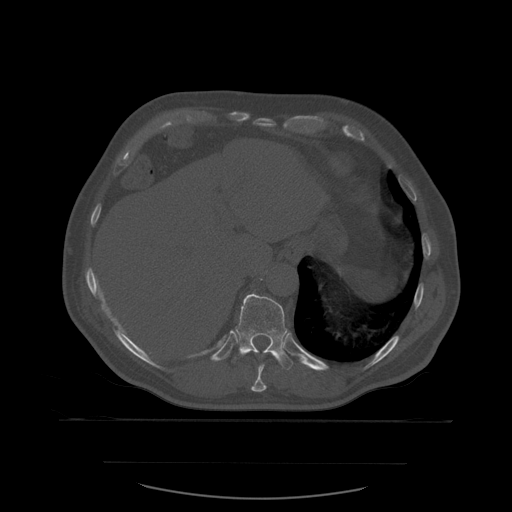
CT including the spine, one axial slice; position 304 of 590 along the scan axis; bone window (W 1800 / L 400 HU); 512 × 512 image matrix. Patient age 71 years. From the clinical record (not read from this slice): primary cancer: lung; vertebrae with lytic lesions (as recorded): T1, T2, L5, S1.
Outlined on this slice (semi-automatically segmented with operator editing):
- T10 vertebra: bounding box [x1, y1, x2, y2] px = [252, 364, 267, 392]
- T11 vertebra: [232, 294, 294, 370]